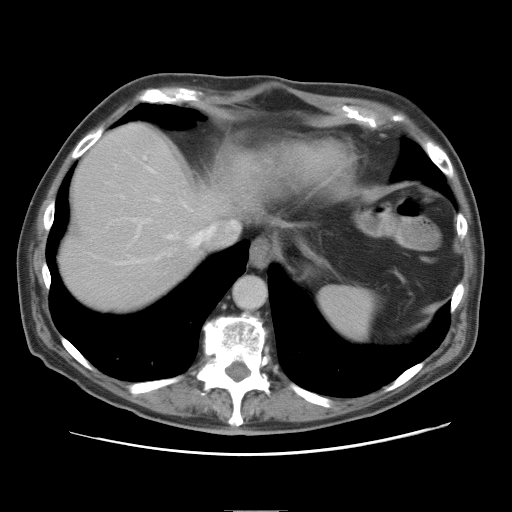
Contrast-enhanced abdominal CT, one axial slice; position 68 of 89 along the scan axis; 120 kVp; soft-tissue window (W 400 / L 40 HU); 512 × 512 image matrix. Male patient, age 69 years. Case-level facts recorded for this patient, not image findings: diagnosis: colorectal cancer liver metastases, imaged before liver resection; multiple liver metastases: no; largest metastasis: 8.5 cm; disease in both lobes: no.
Outlined on this slice (outlined manually by an expert reader):
- hepatic veins: bounding box (x1, y1, x2, y2) in pixels: (118, 169, 239, 264)
- liver: (58, 123, 226, 313)
- planned liver remnant (the part of the liver to remain after resection): (58, 124, 228, 314)
- portal vein (with intrahepatic branches): (132, 157, 151, 238)